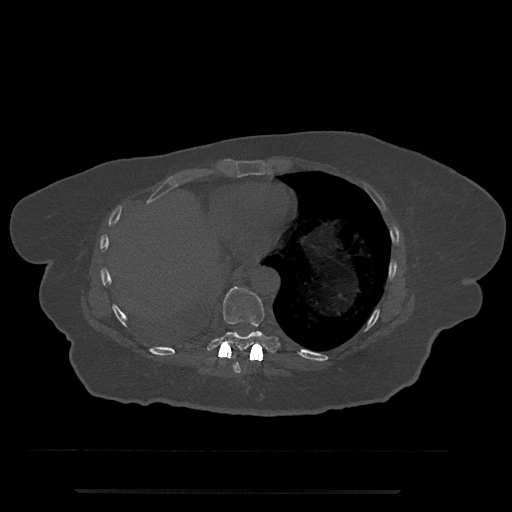
CT including the spine, one axial slice; slice 339 of 797 in the series (ordered by position); reconstruction kernel Br40s/3; 120 kVp; bone window (W 1800 / L 400 HU); 0.5 mm slice thickness; 512 × 512 image matrix. Patient: female, 51 years. From the clinical record (not read from this slice): primary cancer: neuro.
Structures marked on this image (semi-automatic segmentation, software-assisted and operator-edited):
- T8 vertebra: bounding box <234,353,241,373> (left, top, right, bottom; pixels)
- T9 vertebra: <207,286,278,358>